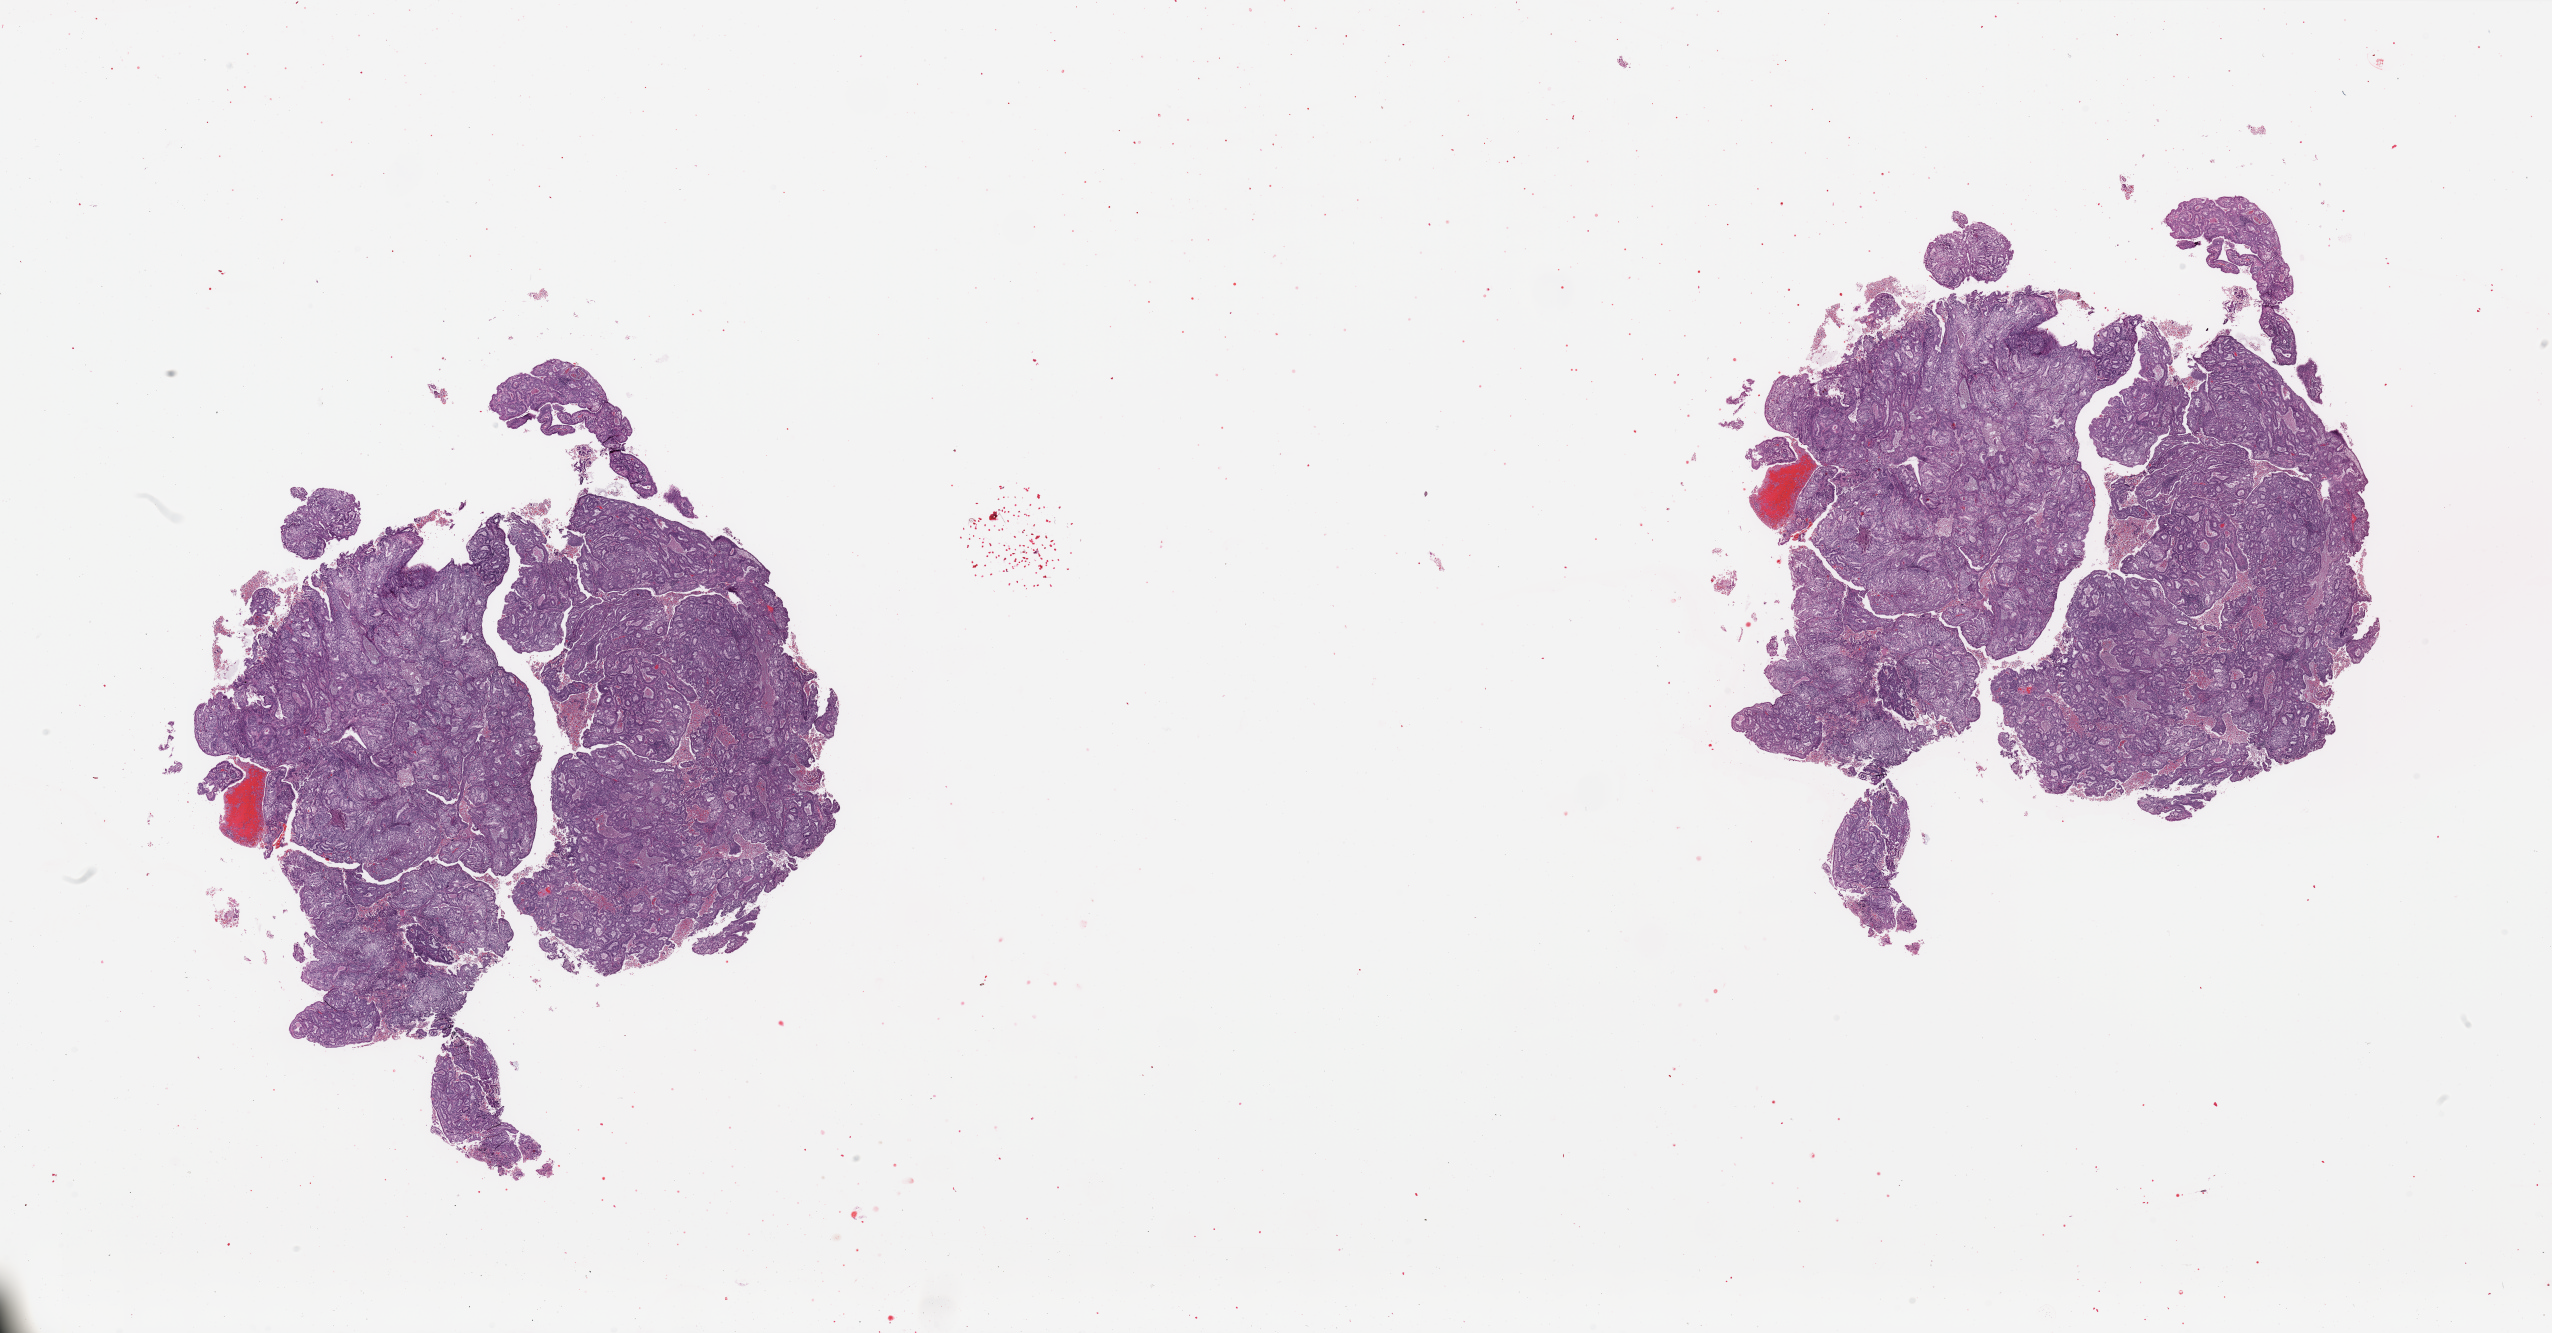
Whole-slide histology image, H&E — a low-resolution overview of the entire scanned area, about 40.4 x 21.1 mm. Uterus, tumour tissue. 72-year-old female patient.
Diagnosis: Endometrioid adenocarcinoma, NOS.